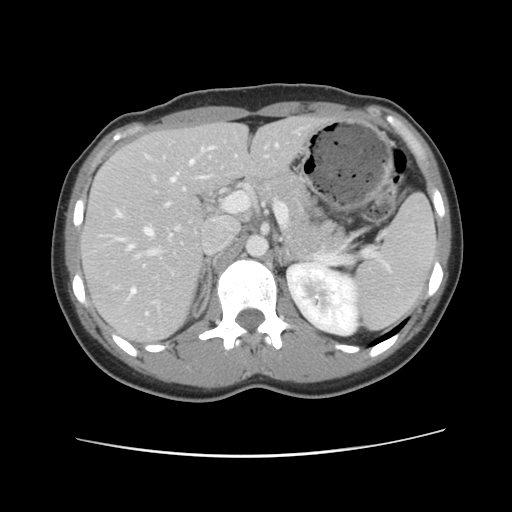
Contrast-enhanced abdominal CT, one axial slice; position 63 of 134 along the scan axis; 120 kVp; intravenous contrast given; soft-tissue window (W 400 / L 40 HU); 2.5 mm slice thickness; 512 × 512 image matrix, field of view 339 × 339 mm. Female patient, age 33 years. From the clinical record (not read from this slice): diagnosis: colorectal cancer liver metastases, imaged before liver resection; multiple liver metastases: yes; largest metastasis: 4.5 cm; disease in both lobes: yes.
Outlined on this slice (expert manual segmentation):
- hepatic veins: bounding box [x1, y1, x2, y2] px = [116, 144, 278, 315]
- liver: [82, 117, 322, 343]
- planned liver remnant (the part of the liver to remain after resection): [82, 117, 323, 343]
- portal vein (with intrahepatic branches): [134, 195, 235, 304]